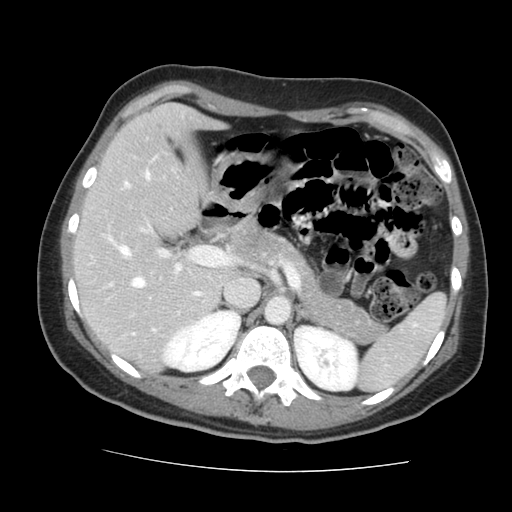
Contrast-enhanced abdominal CT, one axial slice; slice 92 of 144 in the series (ordered by position); 120 kVp; soft-tissue window (W 400 / L 40 HU); 2.5 mm slice thickness; 512 × 512 image matrix. Female patient, age 46 years. Case-level facts recorded for this patient, not image findings: diagnosis: colorectal cancer liver metastases, imaged before liver resection; multiple liver metastases: no; largest metastasis: 2.8 cm; disease in both lobes: no.
Annotated regions visible in this slice (expert manual segmentation):
- hepatic veins: bounding box (x1, y1, x2, y2) in pixels: (124, 172, 200, 296)
- liver: (77, 106, 224, 369)
- planned liver remnant (the part of the liver to remain after resection): (77, 106, 224, 369)
- portal vein (with intrahepatic branches): (119, 225, 226, 331)